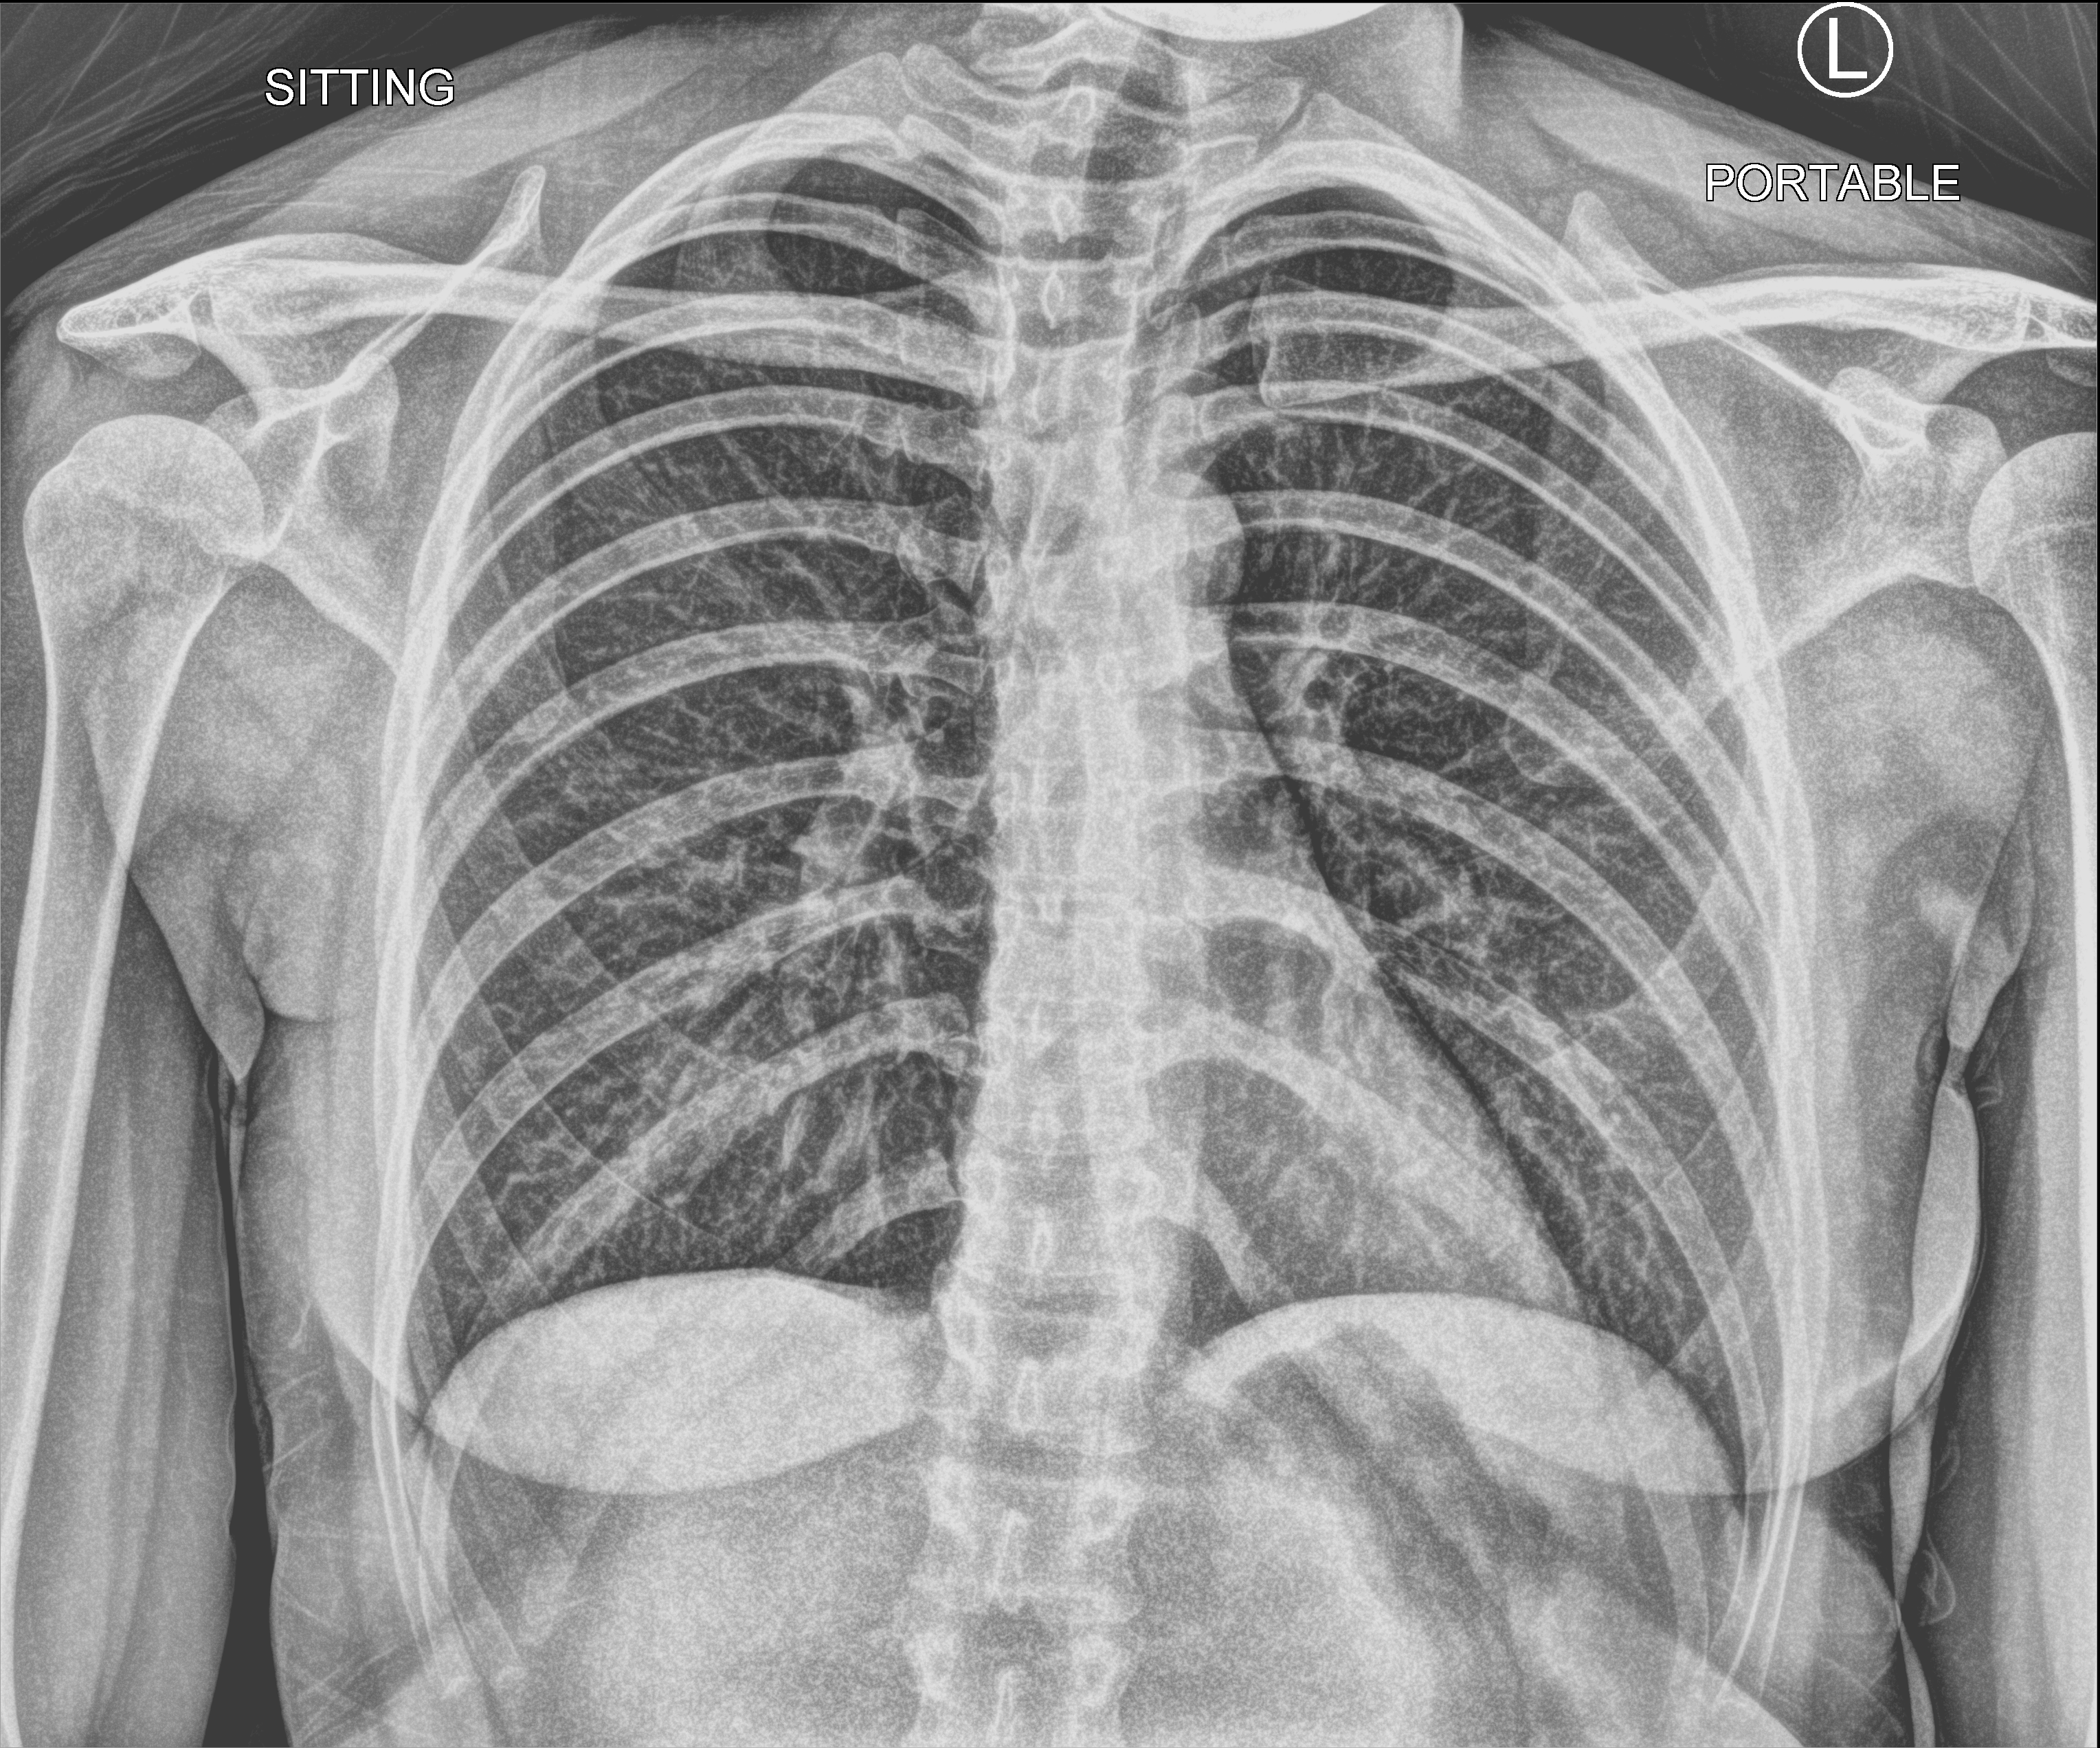
Bedside chest radiograph (computed radiography), anteroposterior (AP) projection. Patient hospitalised with COVID-19; female, aged 18–59 years.
From the hospital-stay record, not from the radiograph (when in the stay this image was taken is not recorded): length of hospital stay: 1 day.